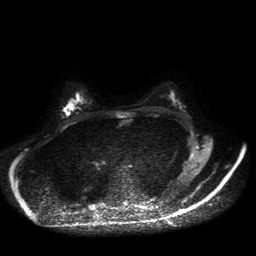
Breast MRI, one axial slice; slice 26 of 50 in the series (ordered by position); diffusion-weighted series; image 2 of 4 stored at this slice position (different b-values; order by instance number); 1.5 T; 4 mm slice thickness; 256 × 256 image matrix, field of view 360 × 360 mm. Female patient.
Annotated regions visible in this slice (expert manual segmentation):
- tumour on diffusion-weighted imaging: bounding box [x1, y1, x2, y2] px = [64, 104, 73, 115]